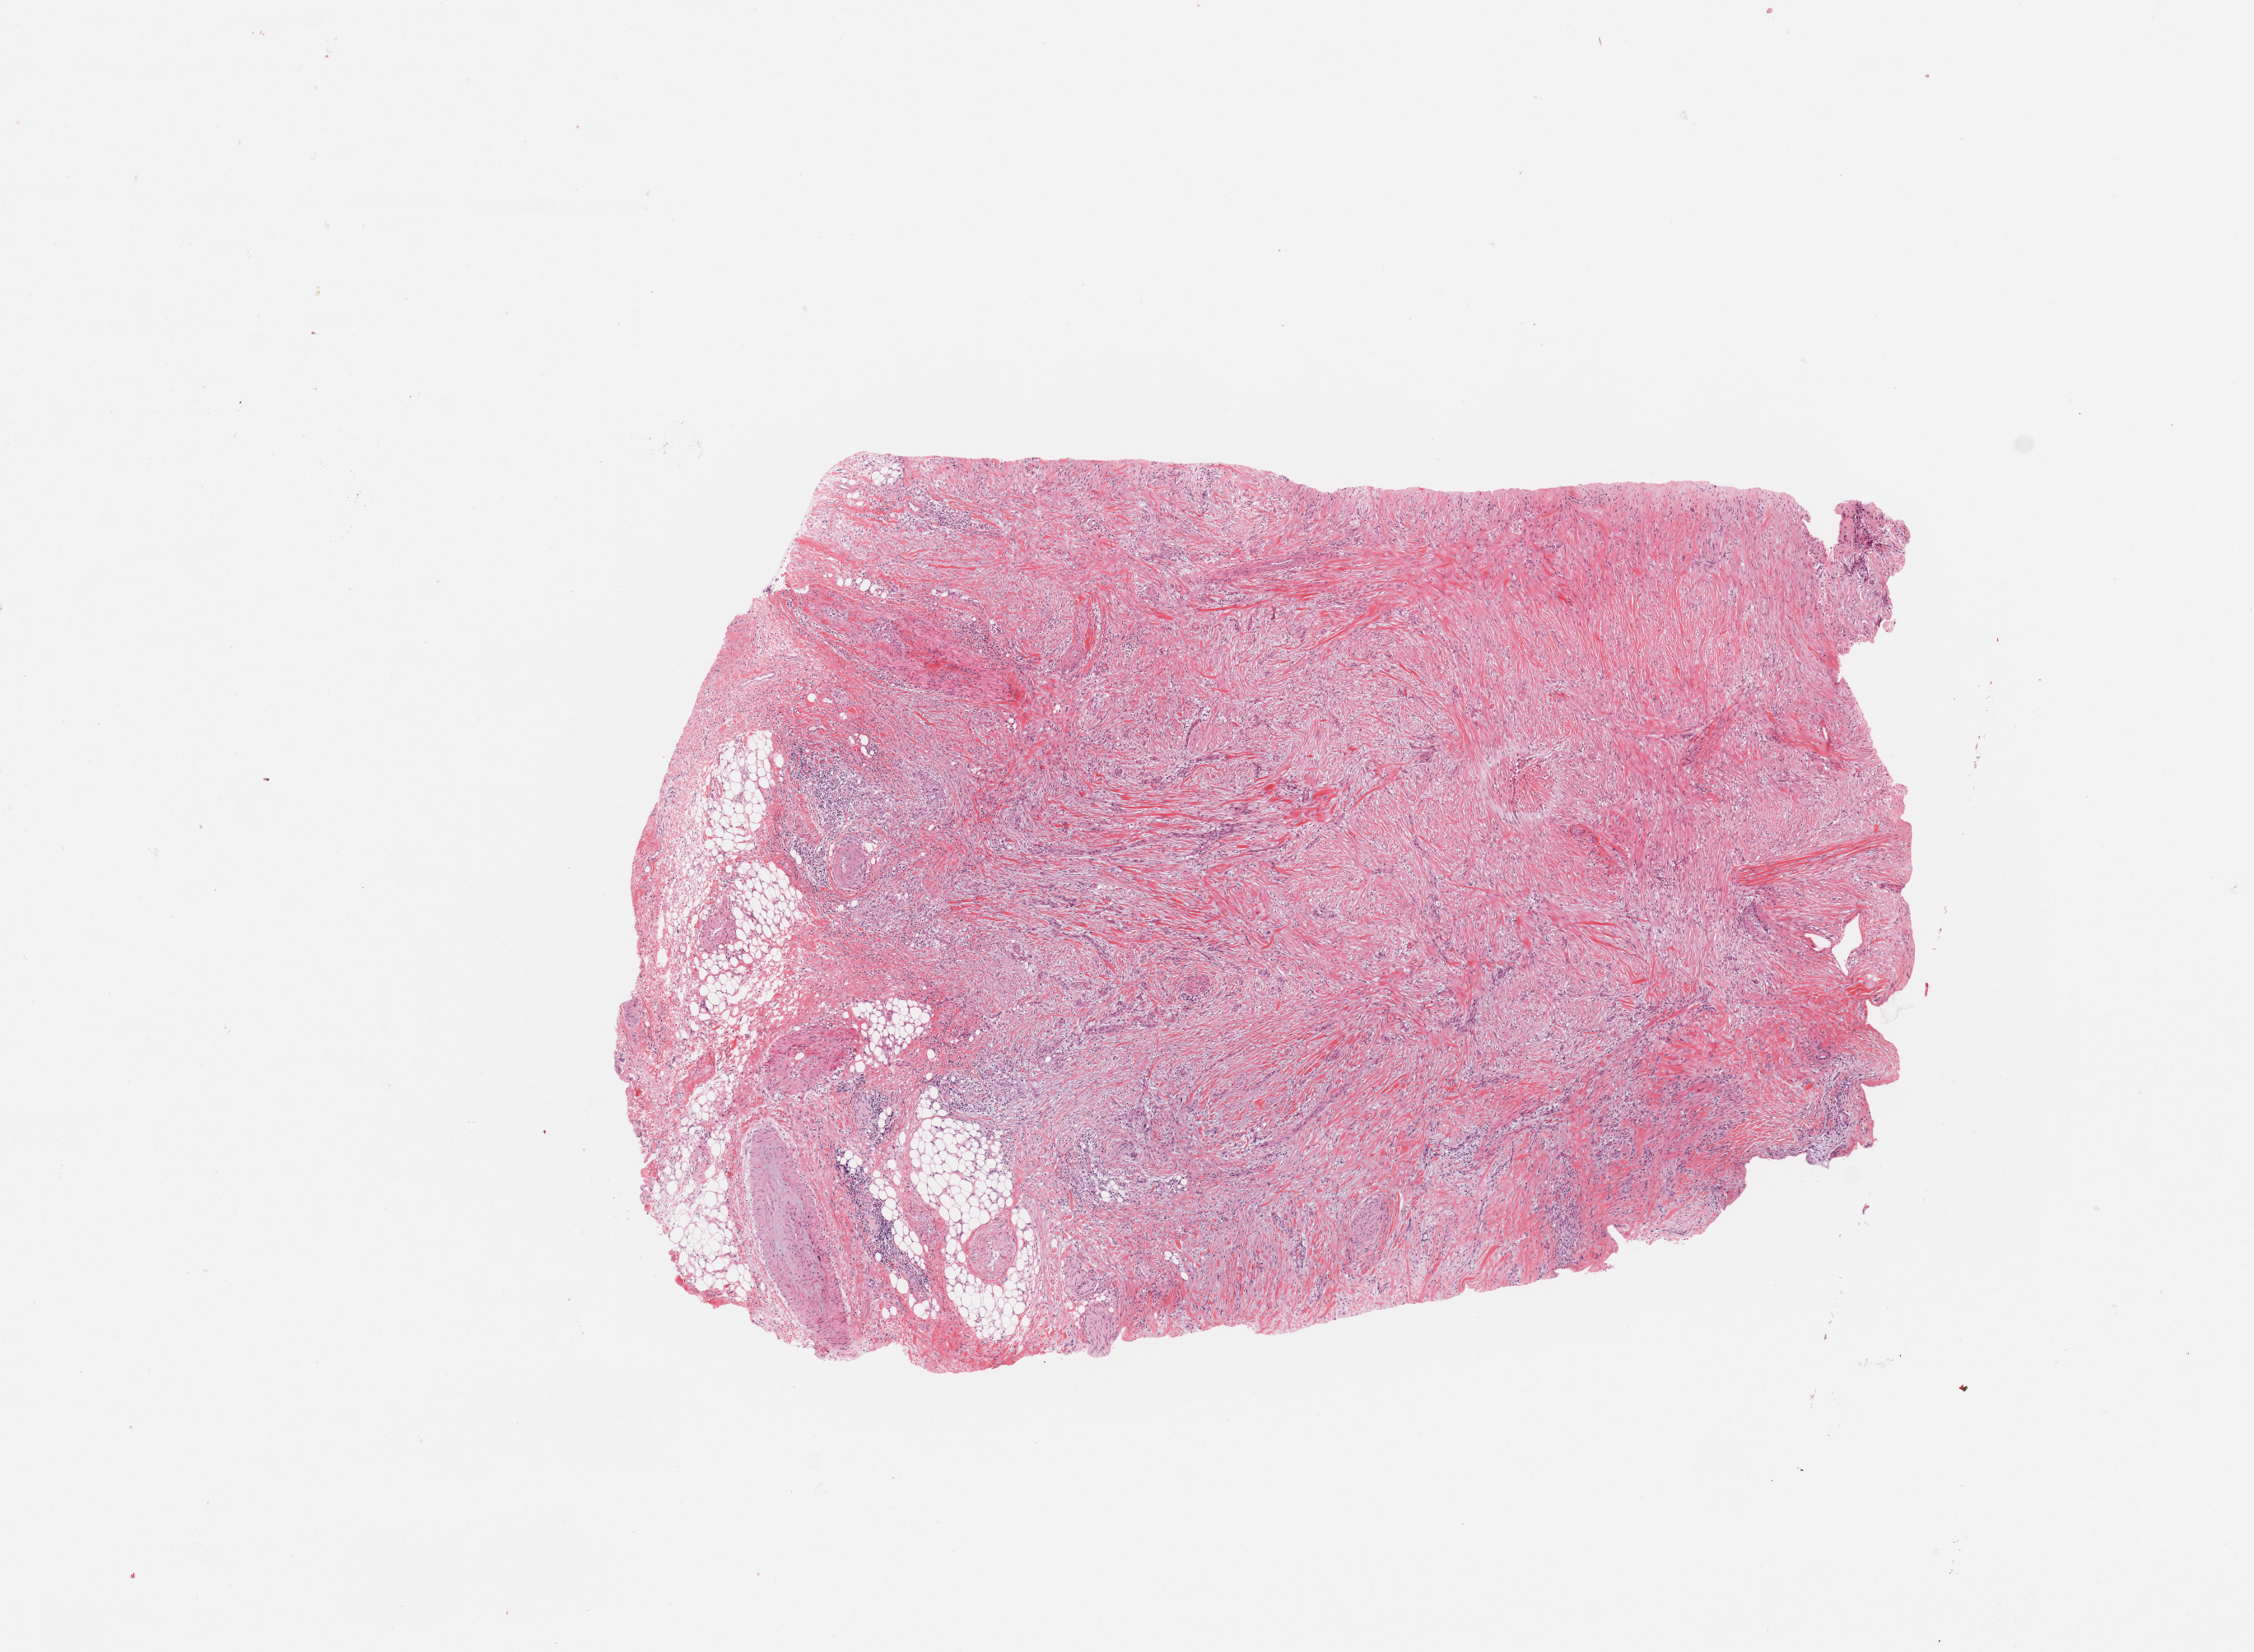
Digitized Hematoxylin and eosin (H&E) stained tissue section (whole slide) — whole scanned area (about 10.8 x 7.9 mm) shown as a low-resolution overview, tumour tissue sample, pancreas. 73-year-old male patient.
Primary tumour site (as recorded): head. Patient diagnosis (cohort enrolment): ductal adenocarcinoma (pancreas).